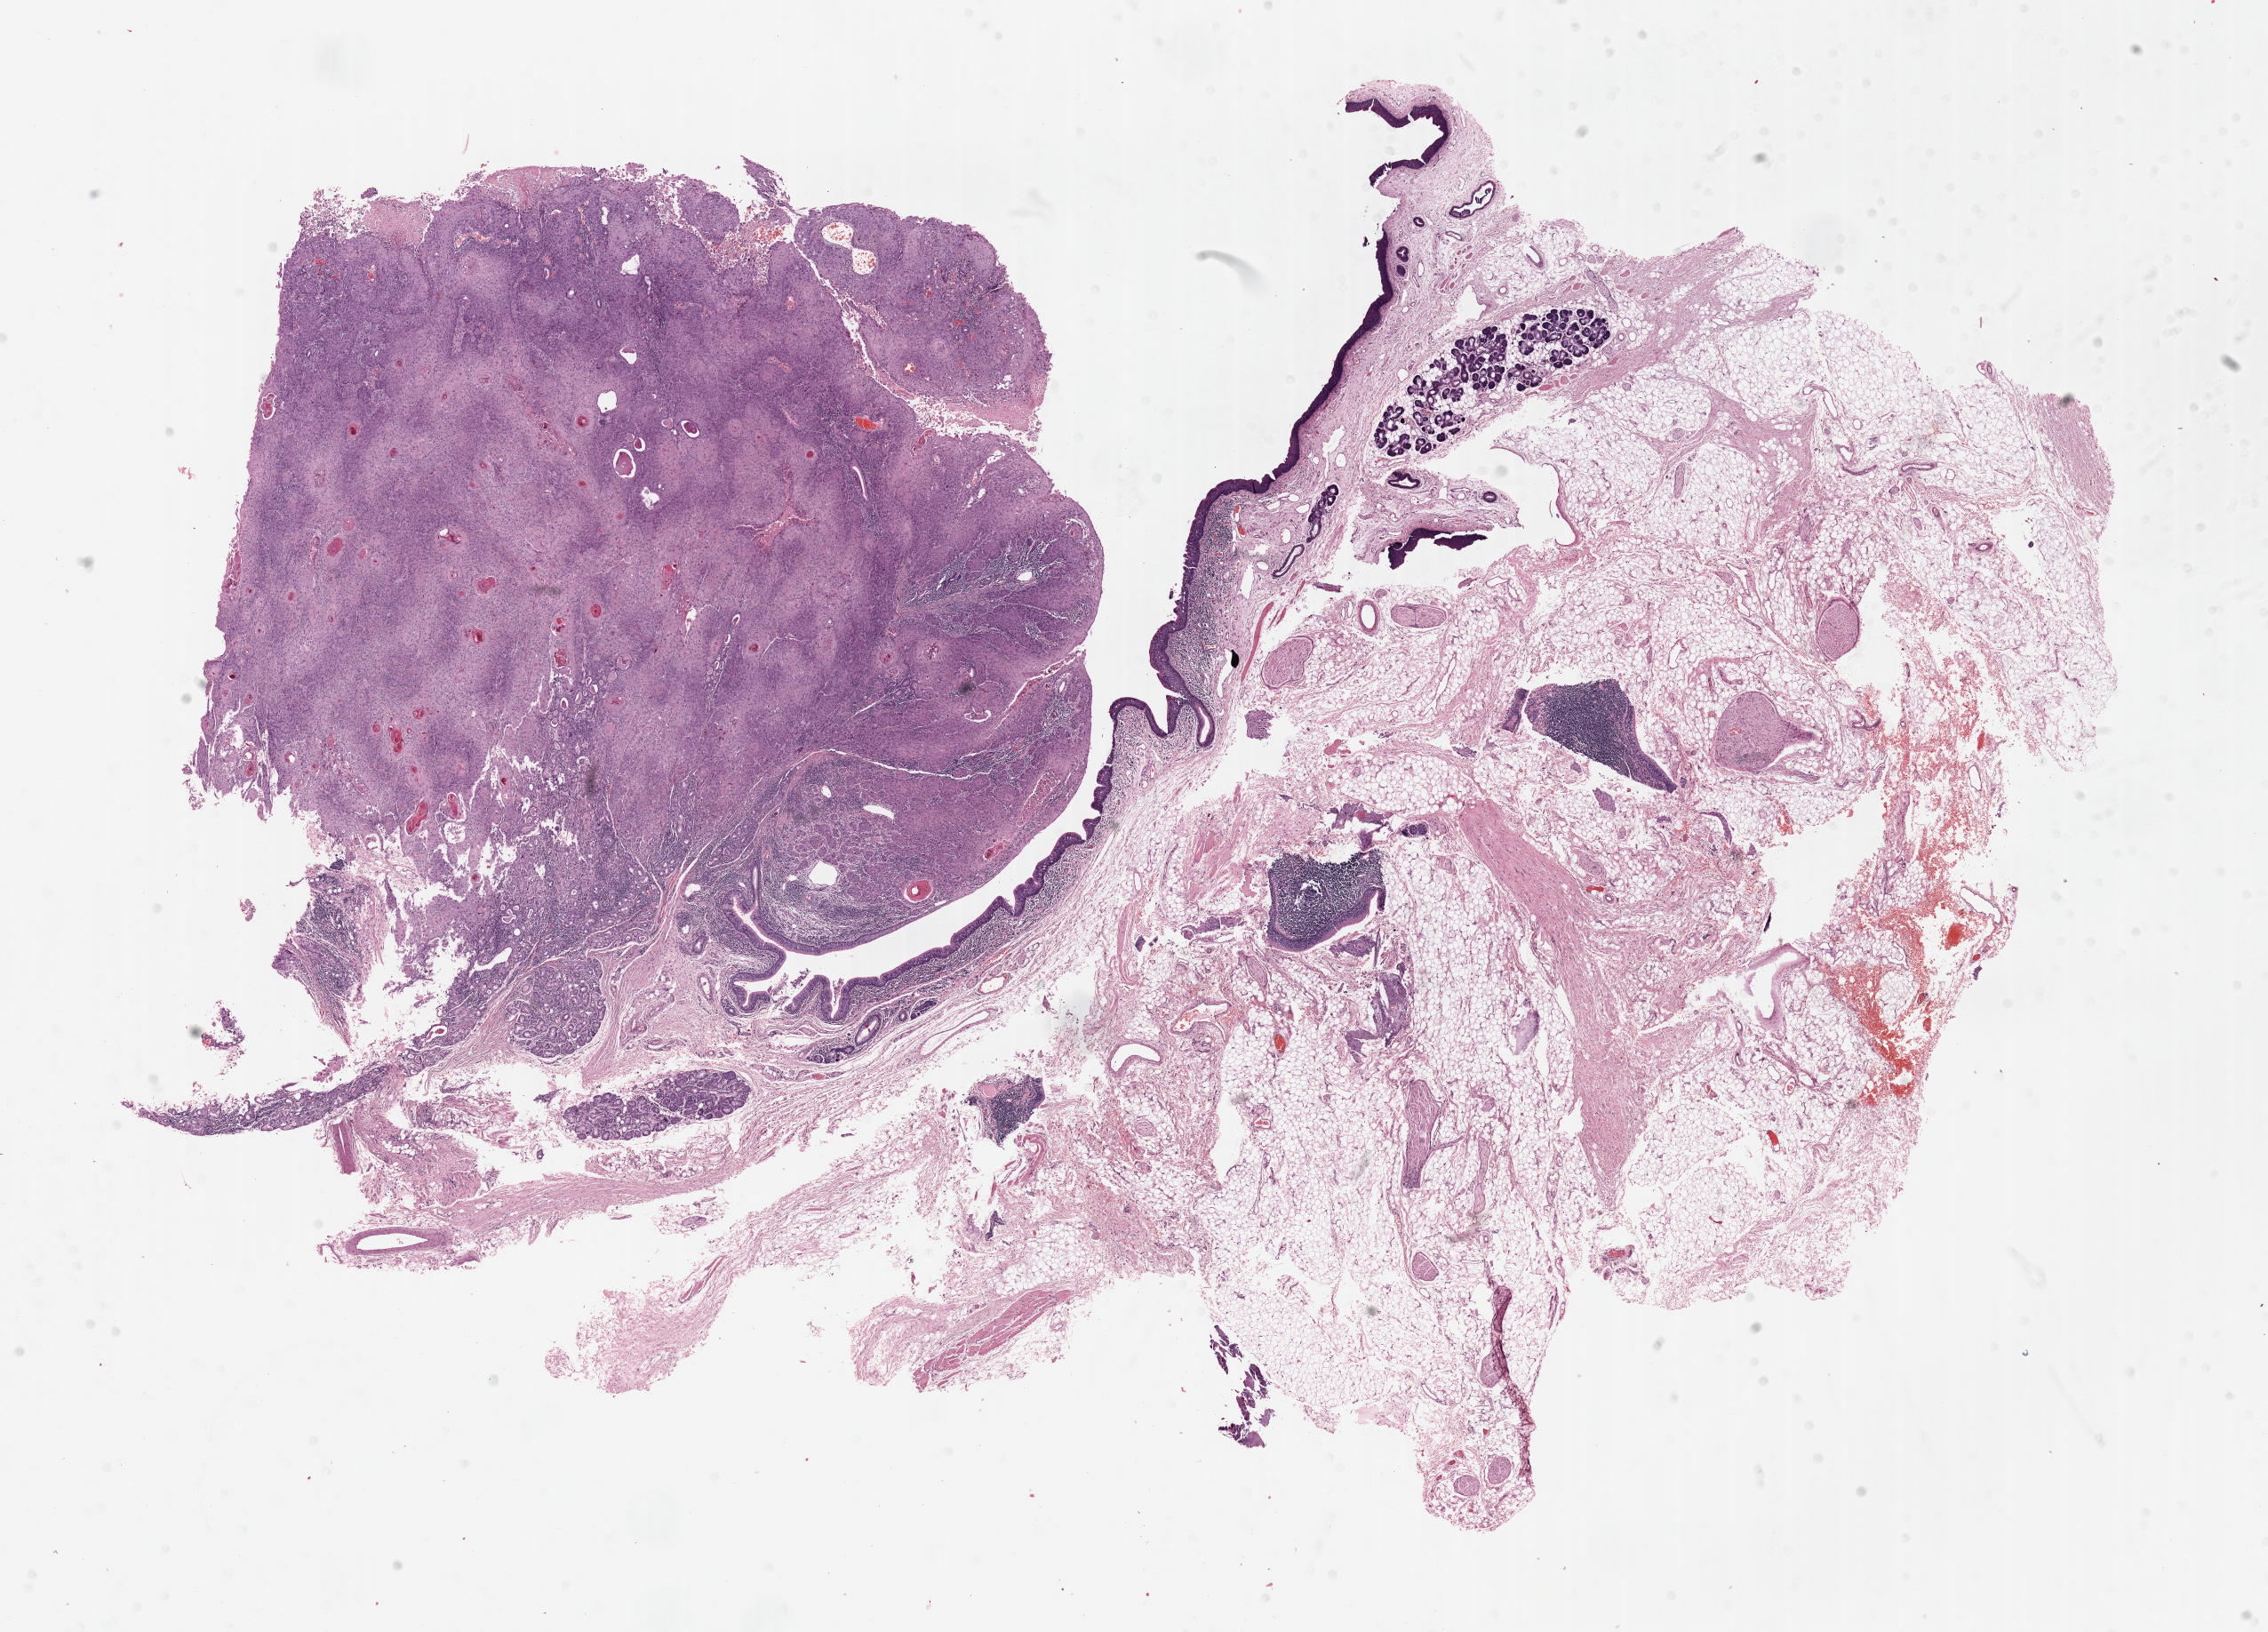
Whole-slide histology image, H&E — shown as a low-resolution overview of the whole scanned area (about 20.6 x 14.8 mm, slide scanned at 40x), FFPE section, head and neck, primary tumour sample. Male, age 57 years at initial diagnosis. Histologic grade: G3 (poorly differentiated).
Diagnosis: Squamous cell carcinoma, keratinizing, NOS. AJCC pathologic stage: IVA (7th edition).